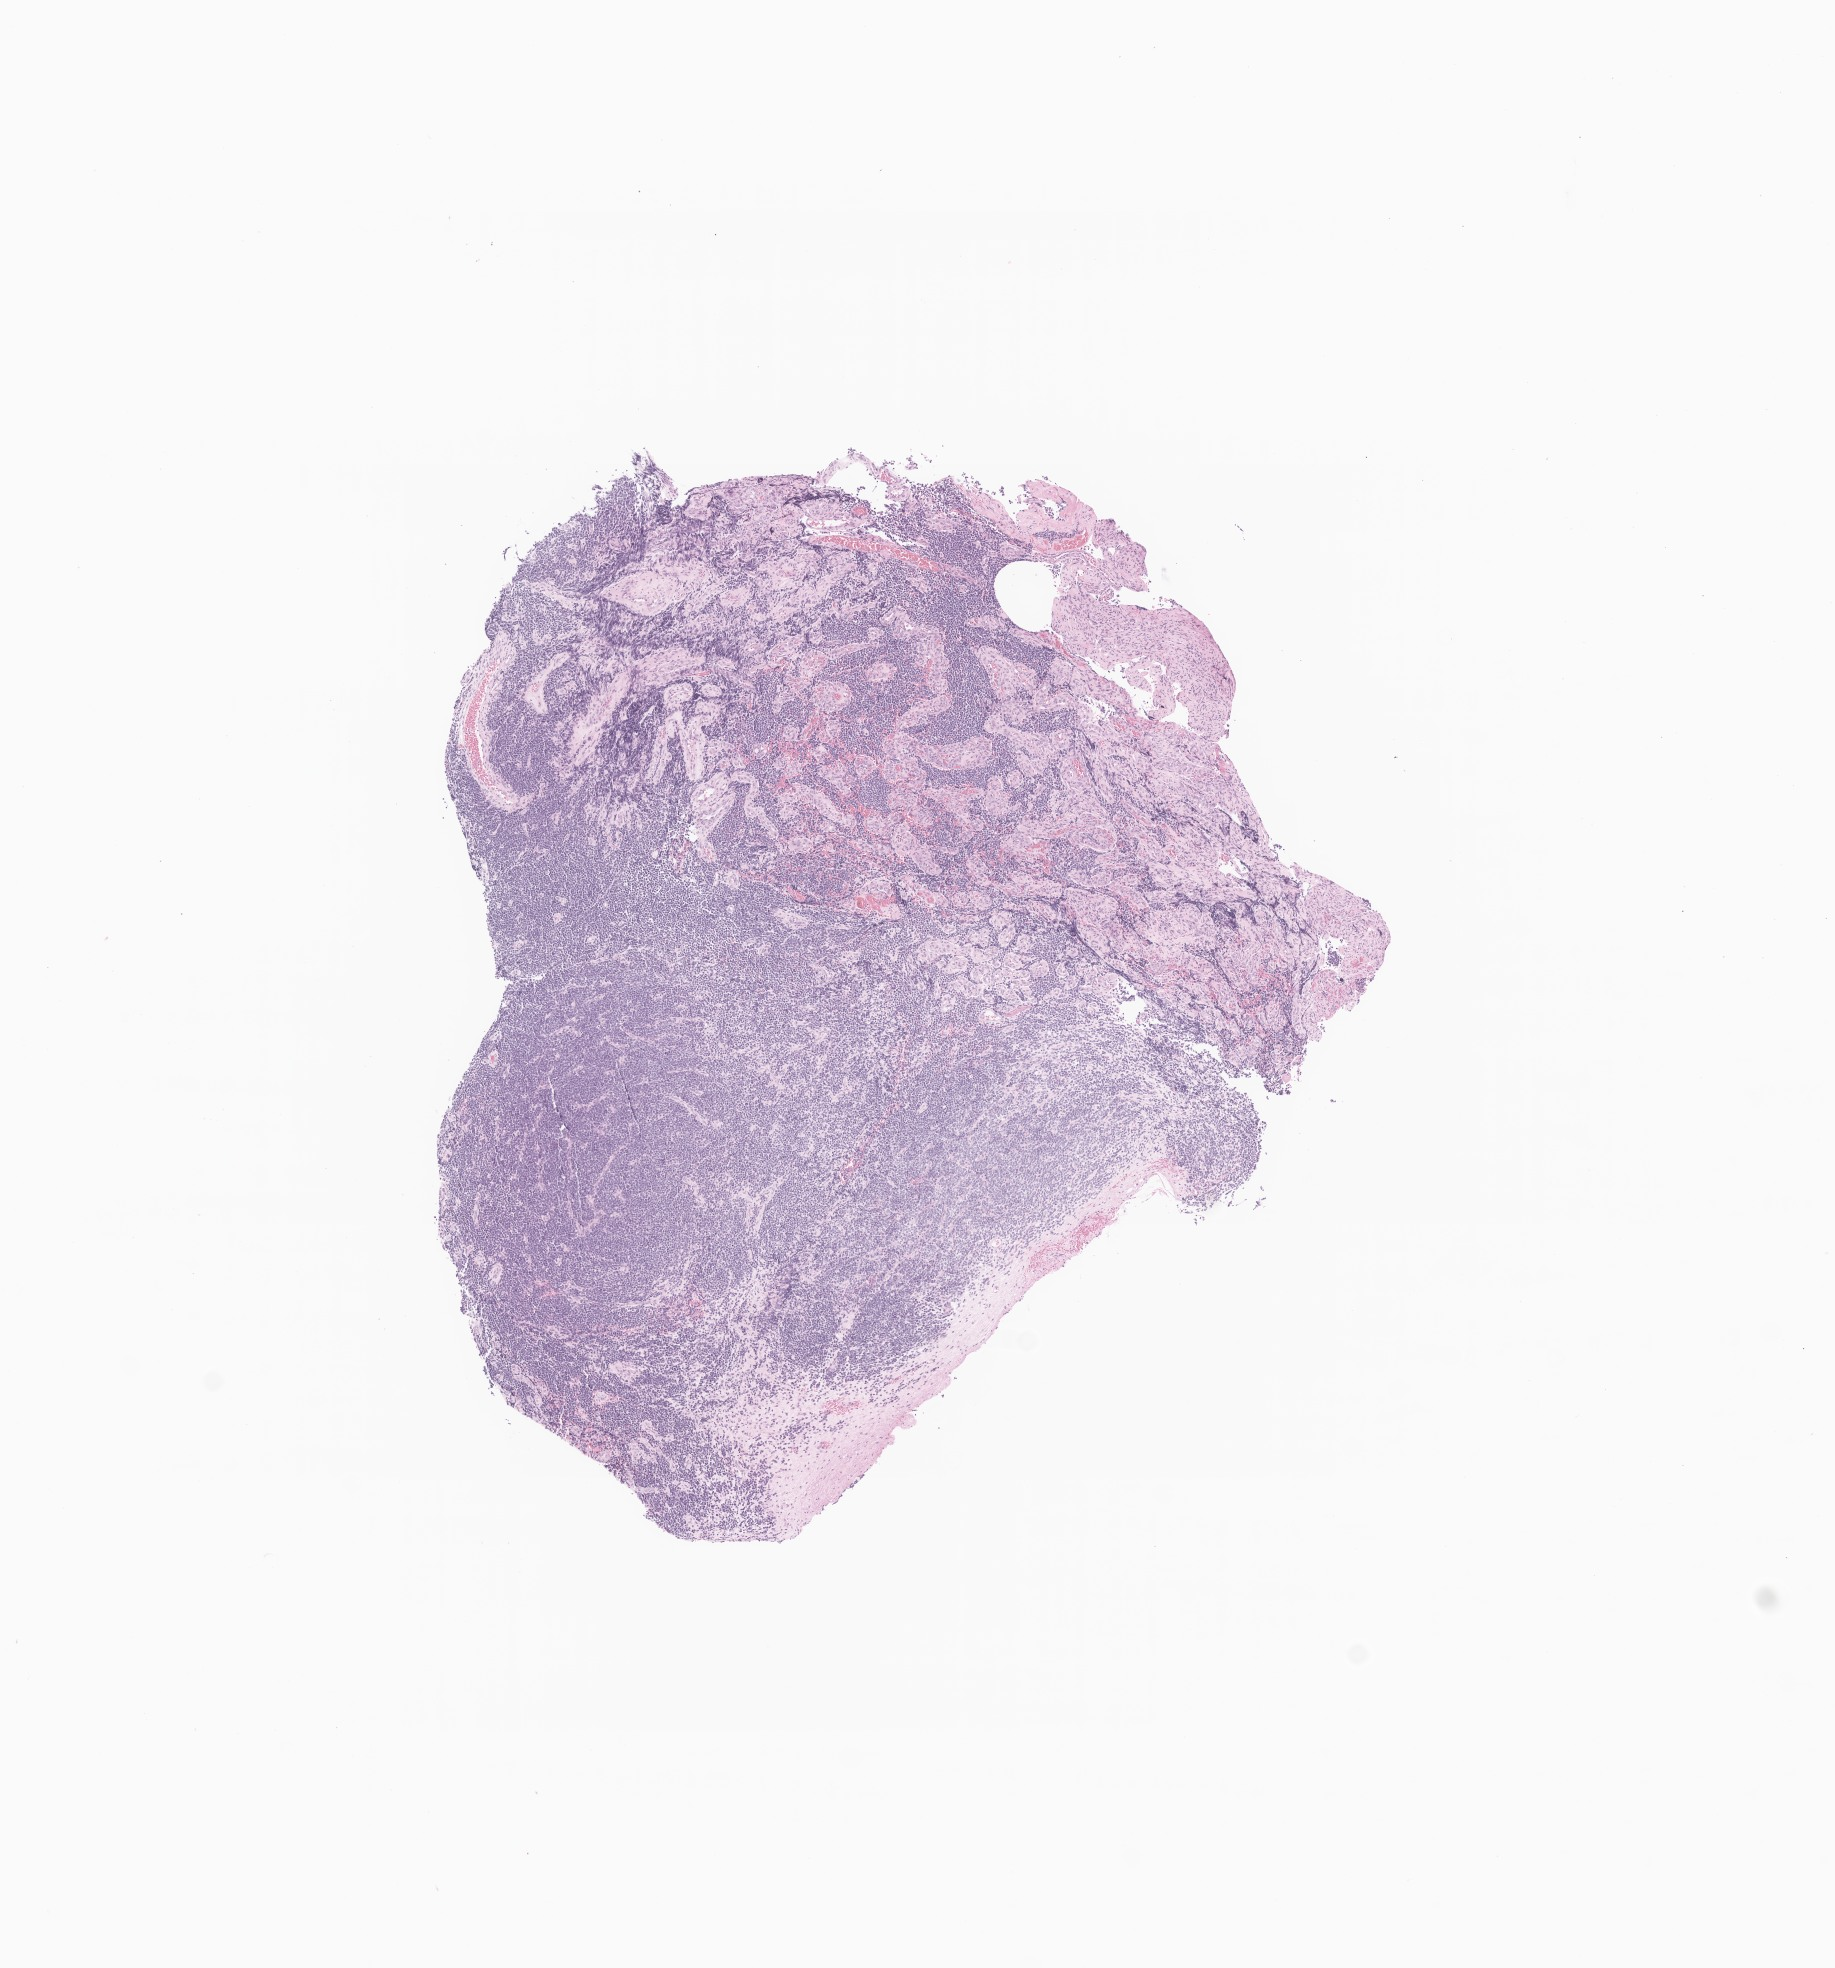
Digitized H&E-stained section of tumor tissue from the brain — low-resolution overview of the scanned area, about 7.7 x 8.3 mm; formalin-fixed, paraffin-embedded (FFPE) tissue. Patient: female, age 70 months (5 years 10 months).
• recorded diagnosis: Medulloblastoma, NOS